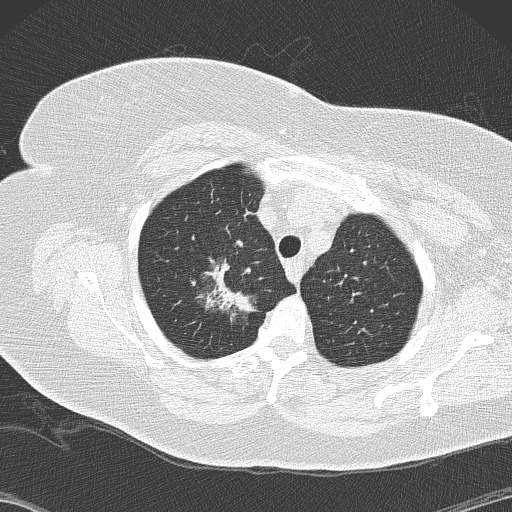
Low-dose screening chest CT, axial slice, second annual screen, lung window (W 1500 / L -600 HU), lung (sharp) reconstruction kernel (B50f), 512 × 512 image matrix. Female, age 72 years at enrolment. Former smoker at enrolment.
Expert reader's lesion annotation, box from (x=180, y=242) to (x=262, y=327) px. The screening reader recorded 4 non-calcified nodules or masses ≥4 mm on this exam (right lower lobe, right lower lobe, right lower lobe, right upper lobe); which of them this box marks is not recorded. Later outcome: lung cancer diagnosed 52 days after this screen — bronchiolo-alveolar adenocarcinoma, NOS, right upper lobe, stage IIIB (AJCC 6th edition), 45 mm at pathology.